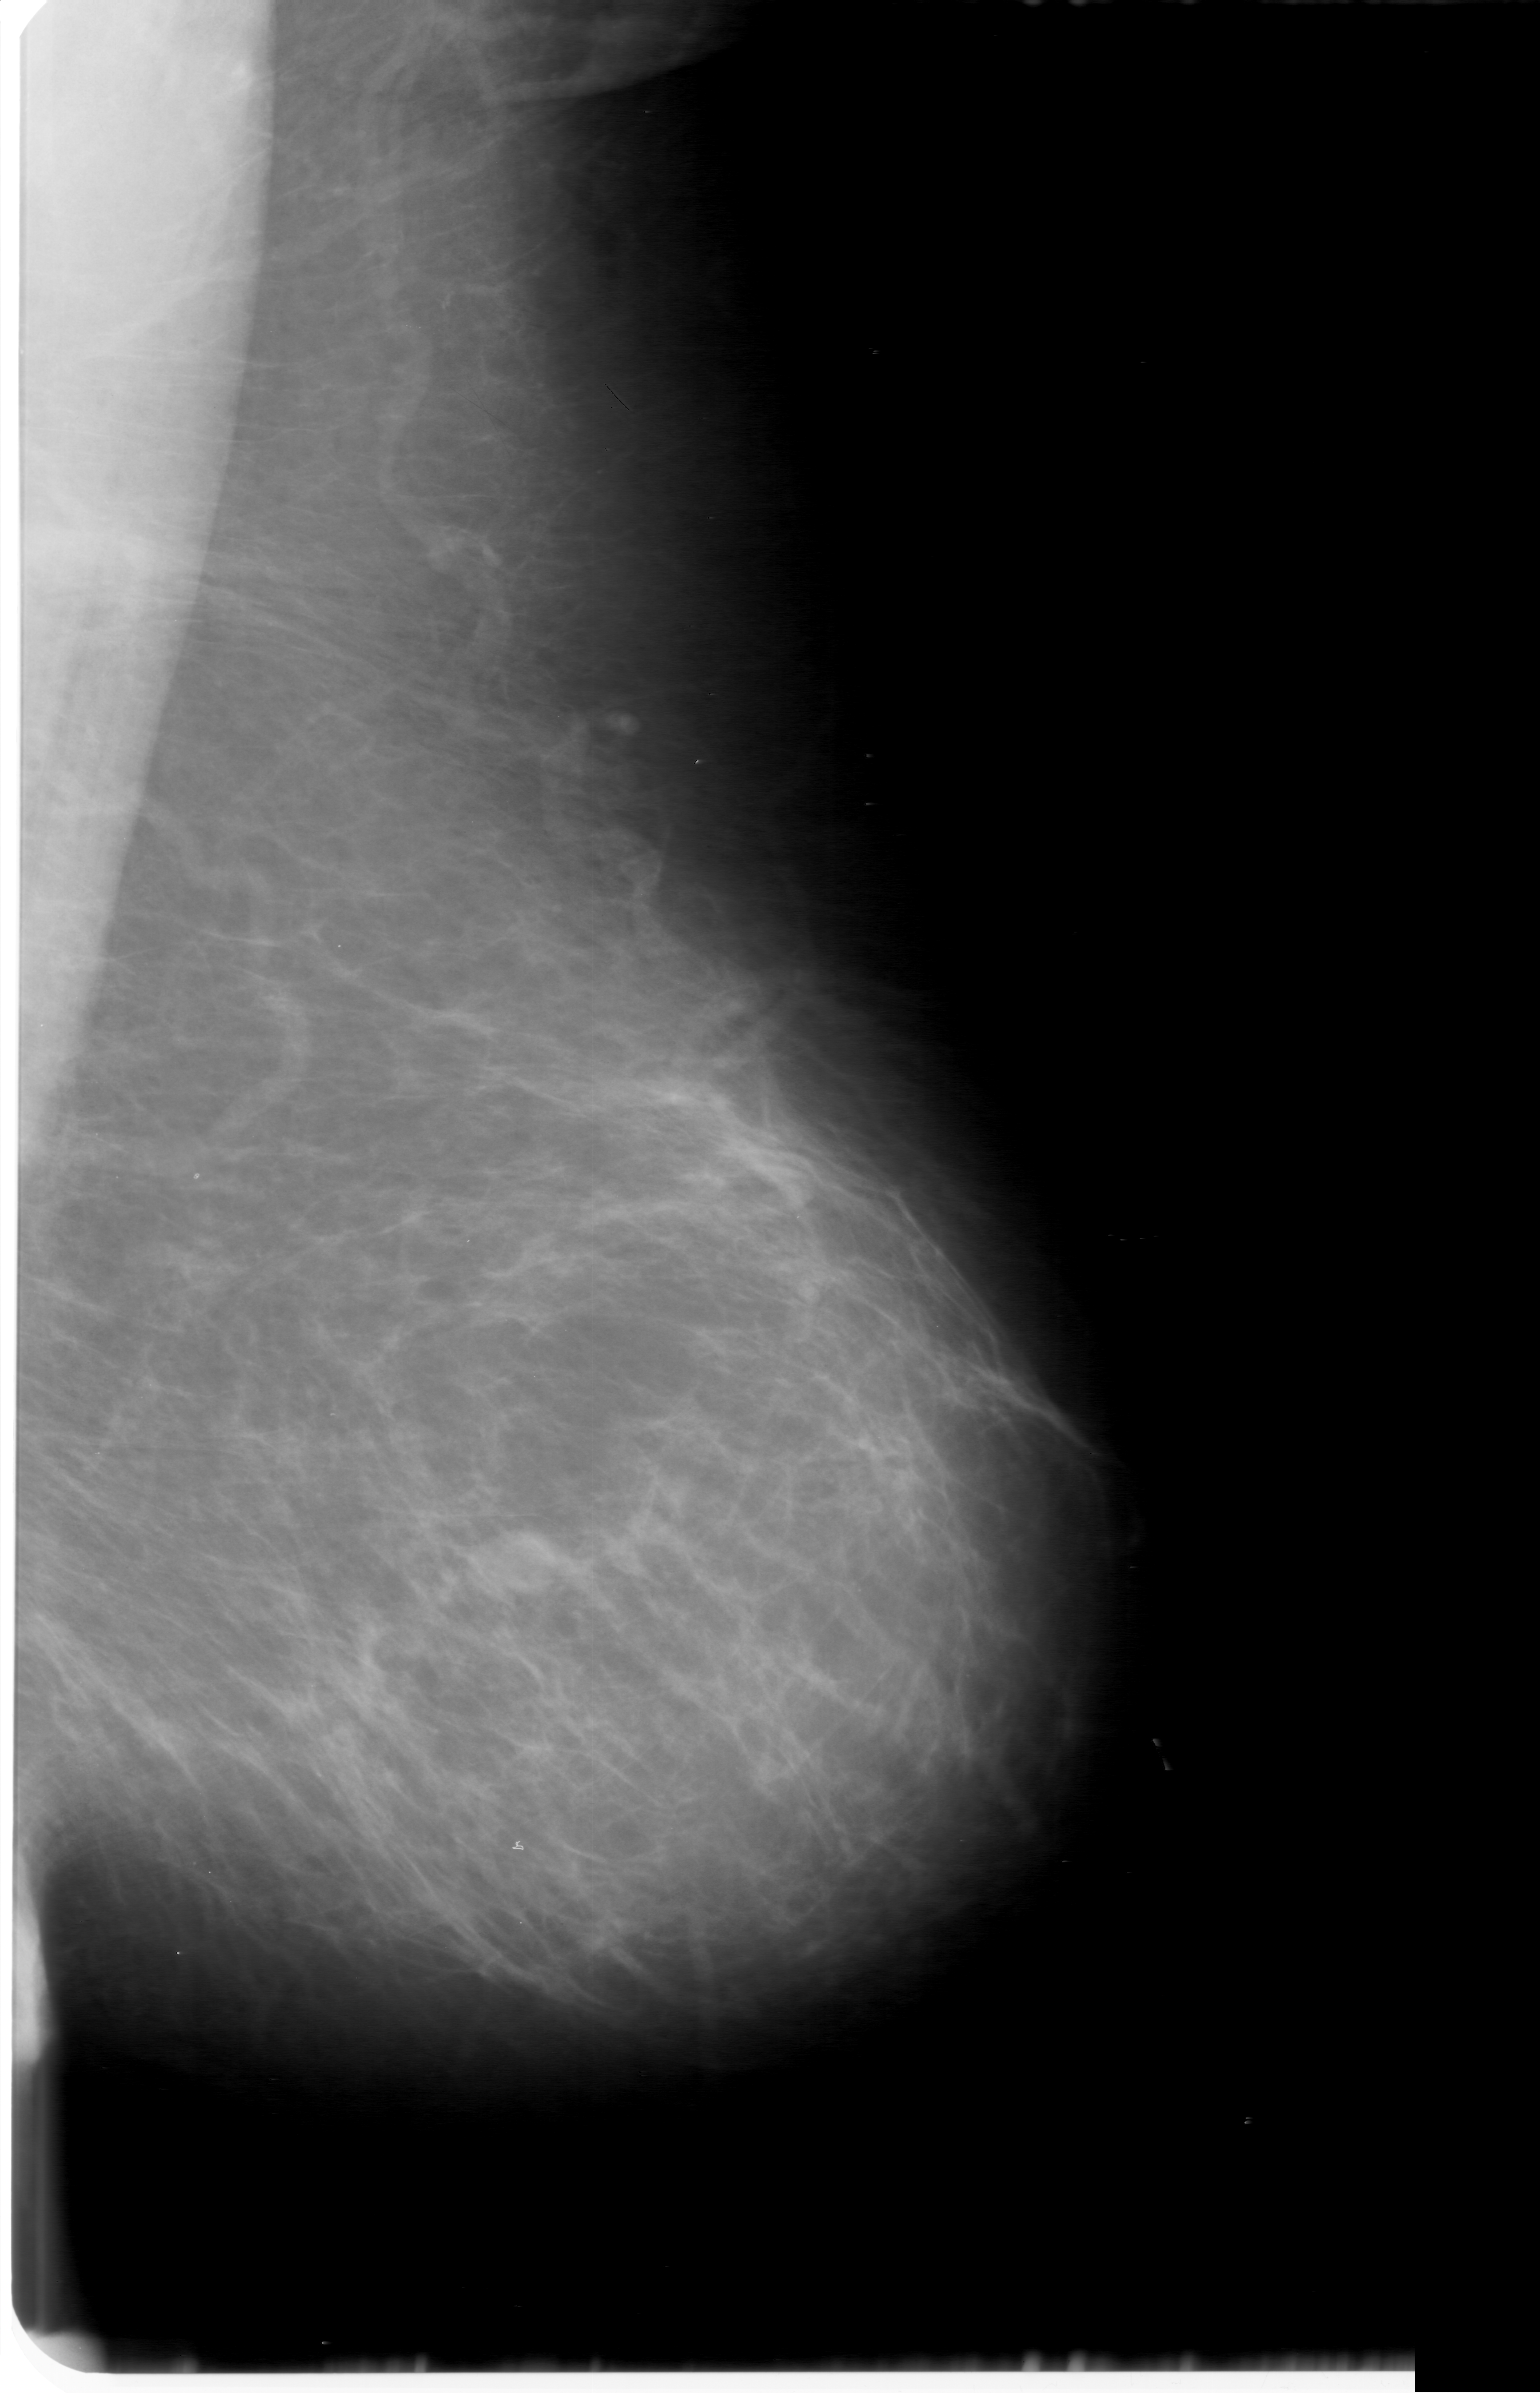
Mammogram (digitized film); left breast; MLO view; BI-RADS breast density category 1 (scale 1–4).
Mass, shape oval, margins obscured; BI-RADS assessment category 3; subtlety rating 4 on a 1 (subtle) to 5 (obvious) scale; pathology (as recorded): malignant.